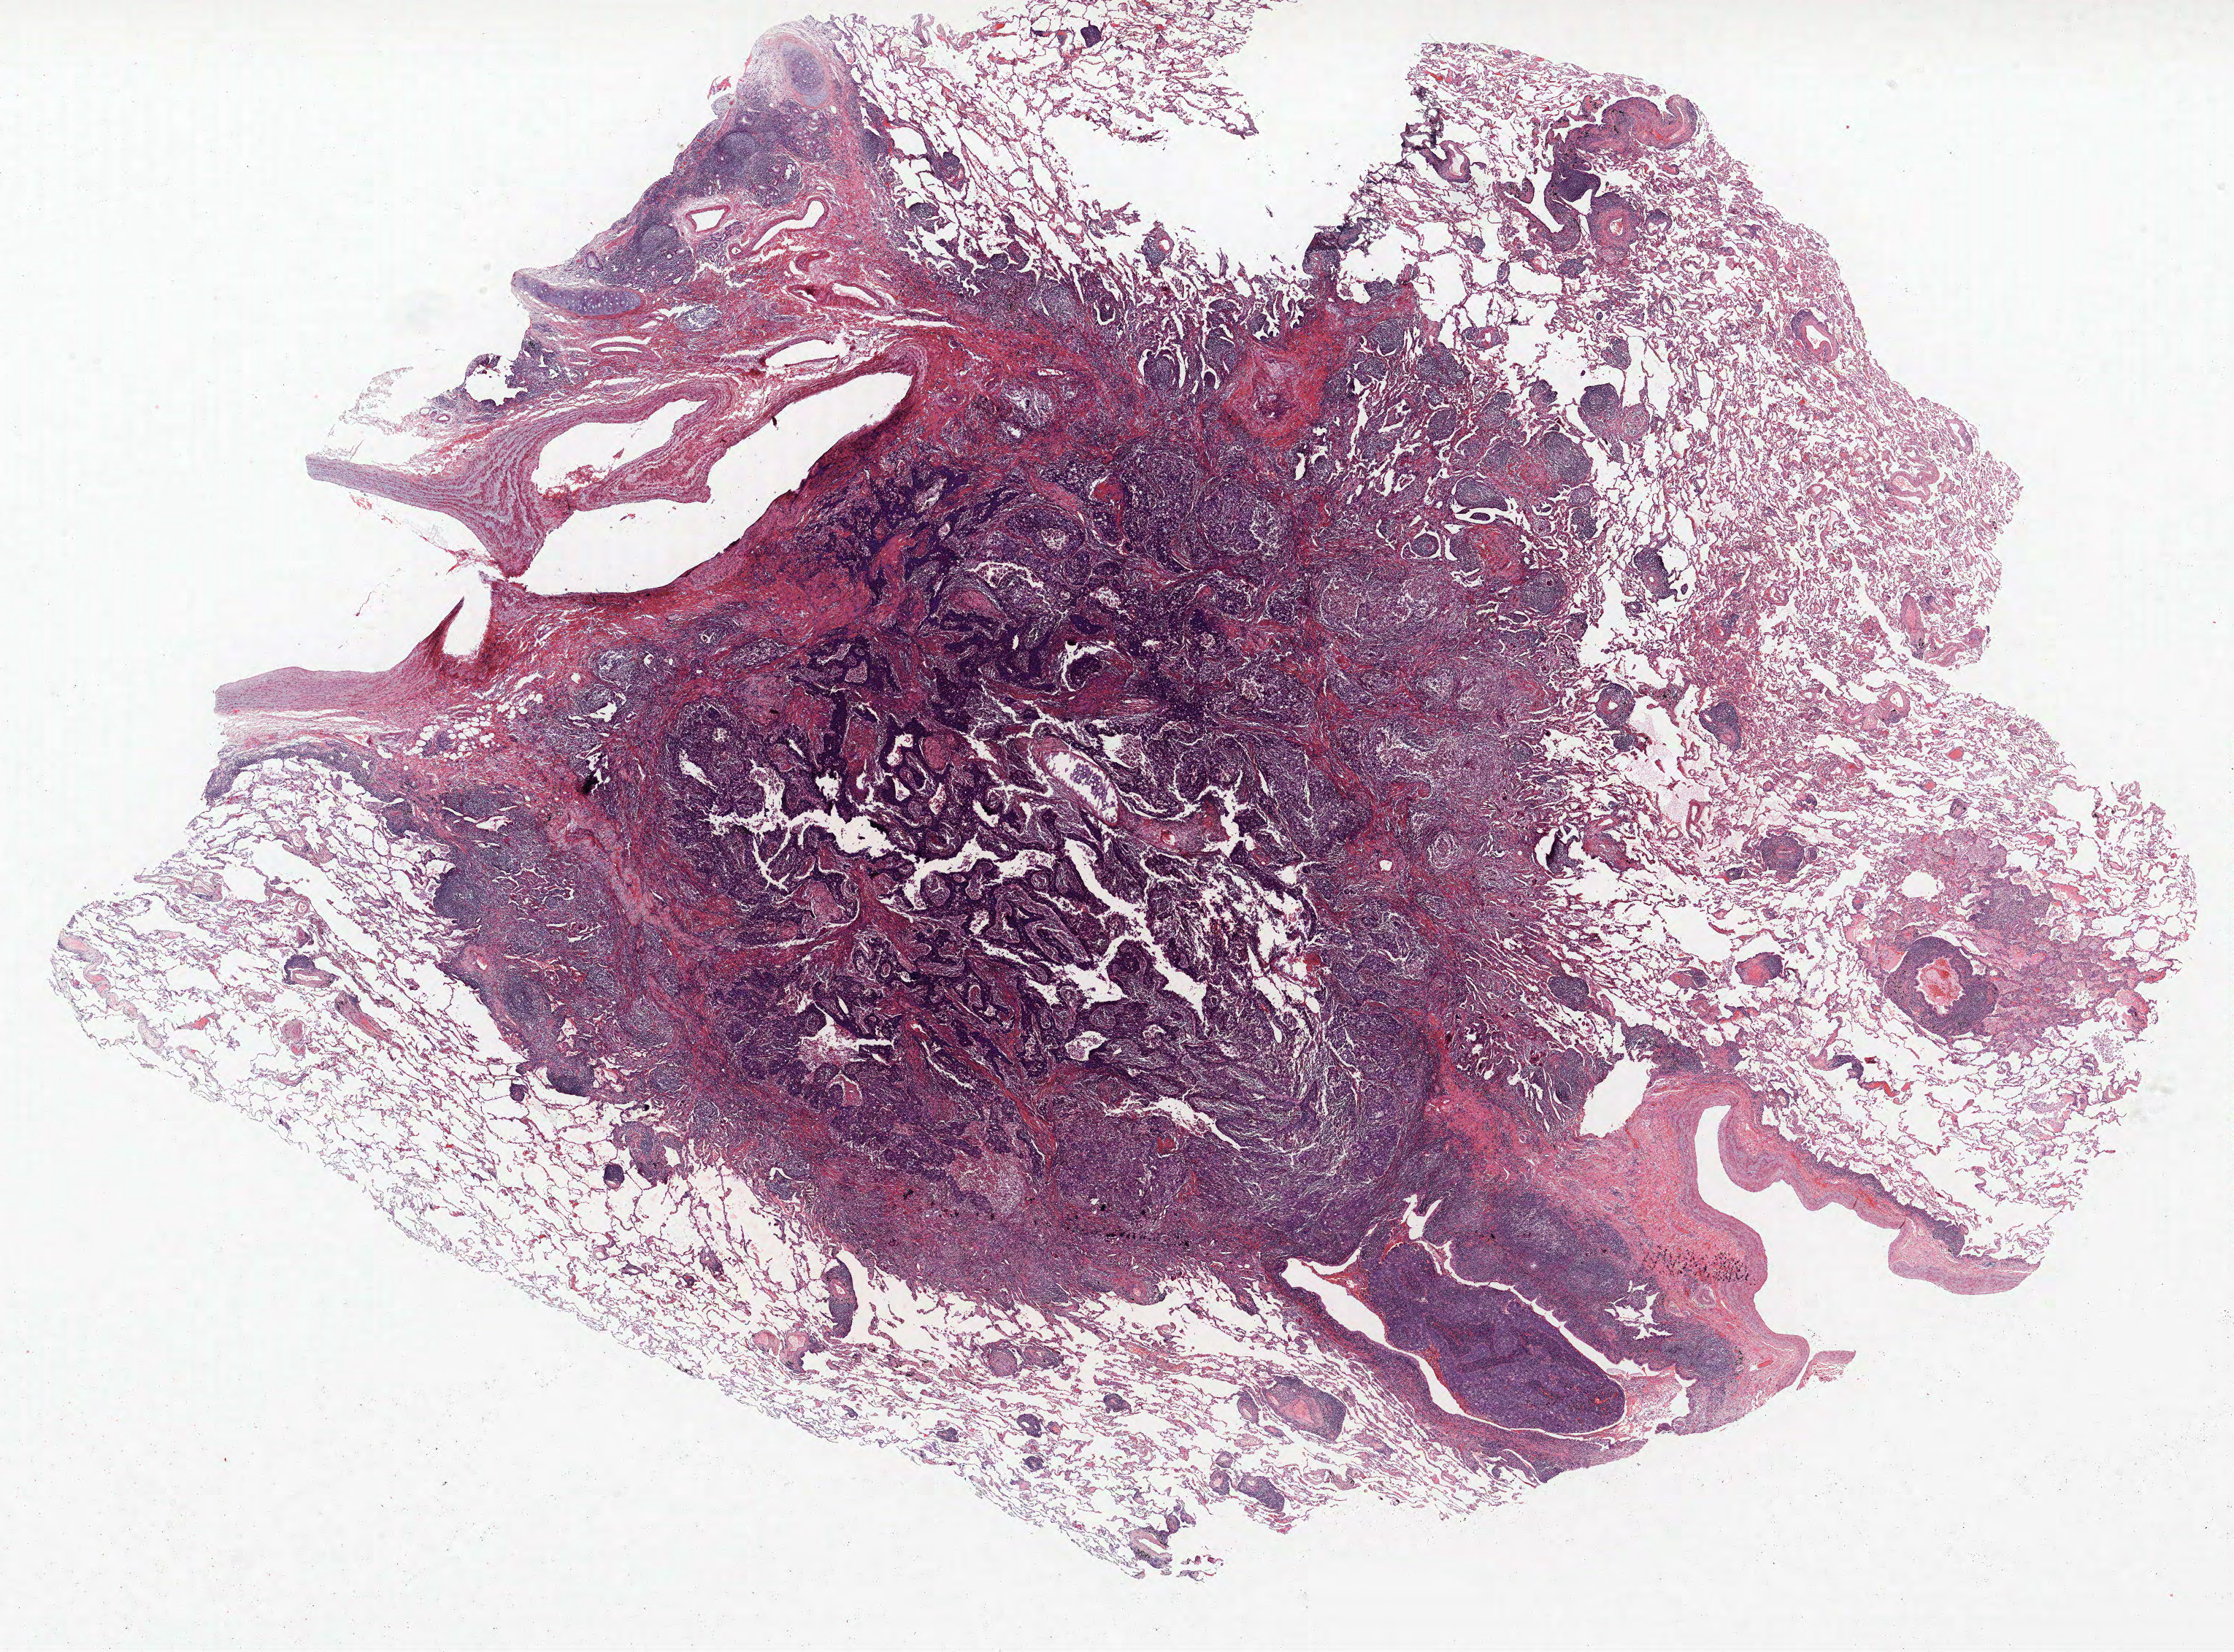
Hematoxylin and eosin (H&E) stained whole-slide image — a low-resolution overview of the entire scanned area, about 24.5 x 18.1 mm, formalin-fixed paraffin-embedded (FFPE) section, lung. Male, age 73 at enrolment. Former smoker at enrolment.
Tumour size (pathology): 30 mm. Stage (AJCC 6th edition): IA. Participant's lung-cancer diagnosis: Non-small cell carcinoma. Primary tumour location (clinical record): right lower lobe.